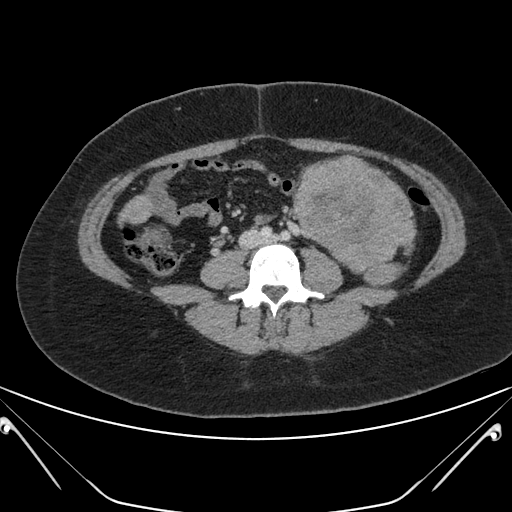
Contrast-enhanced abdominal CT, one axial slice; slice 80 of 168 in the series (ordered by position); 120 kVp; intravenous contrast given; soft-tissue window (W 400 / L 40 HU); 3 mm slice thickness; 512 × 512 image matrix, field of view 394 × 394 mm. Patient: female, 26 years. Case-level facts recorded for this patient, not image findings: diagnosis: adrenocortical carcinoma; tumour side: left adrenal; tumour size at pathology: 28 cm; Ki-67 index: 20 %; stage (as recorded): 2.
Annotated regions visible in this slice (semi-automatically segmented with operator editing):
- mass: bounding box [x1, y1, x2, y2] px = [297, 157, 413, 283]